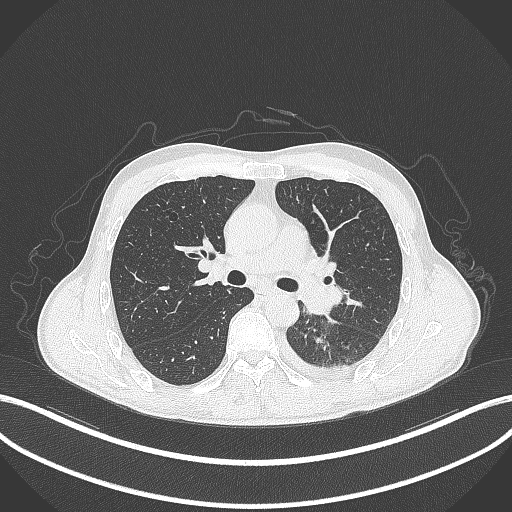
Chest CT, one axial slice; slice 198 of 295 in the series (ordered by position); lung window (W 1500 / L -600 HU); 512 × 512 image matrix, field of view 400 × 400 mm. Patient: male, 47 years. Case-level facts recorded for this patient, not image findings: clinical TNM (as recorded): T3 N1 M1c; histopathological grade: G3.
Structures marked on this image (bounding box drawn by a radiologist):
- lung tumour (recorded histology: small cell carcinoma): bounding box [x1, y1, x2, y2] px = [299, 274, 345, 315]